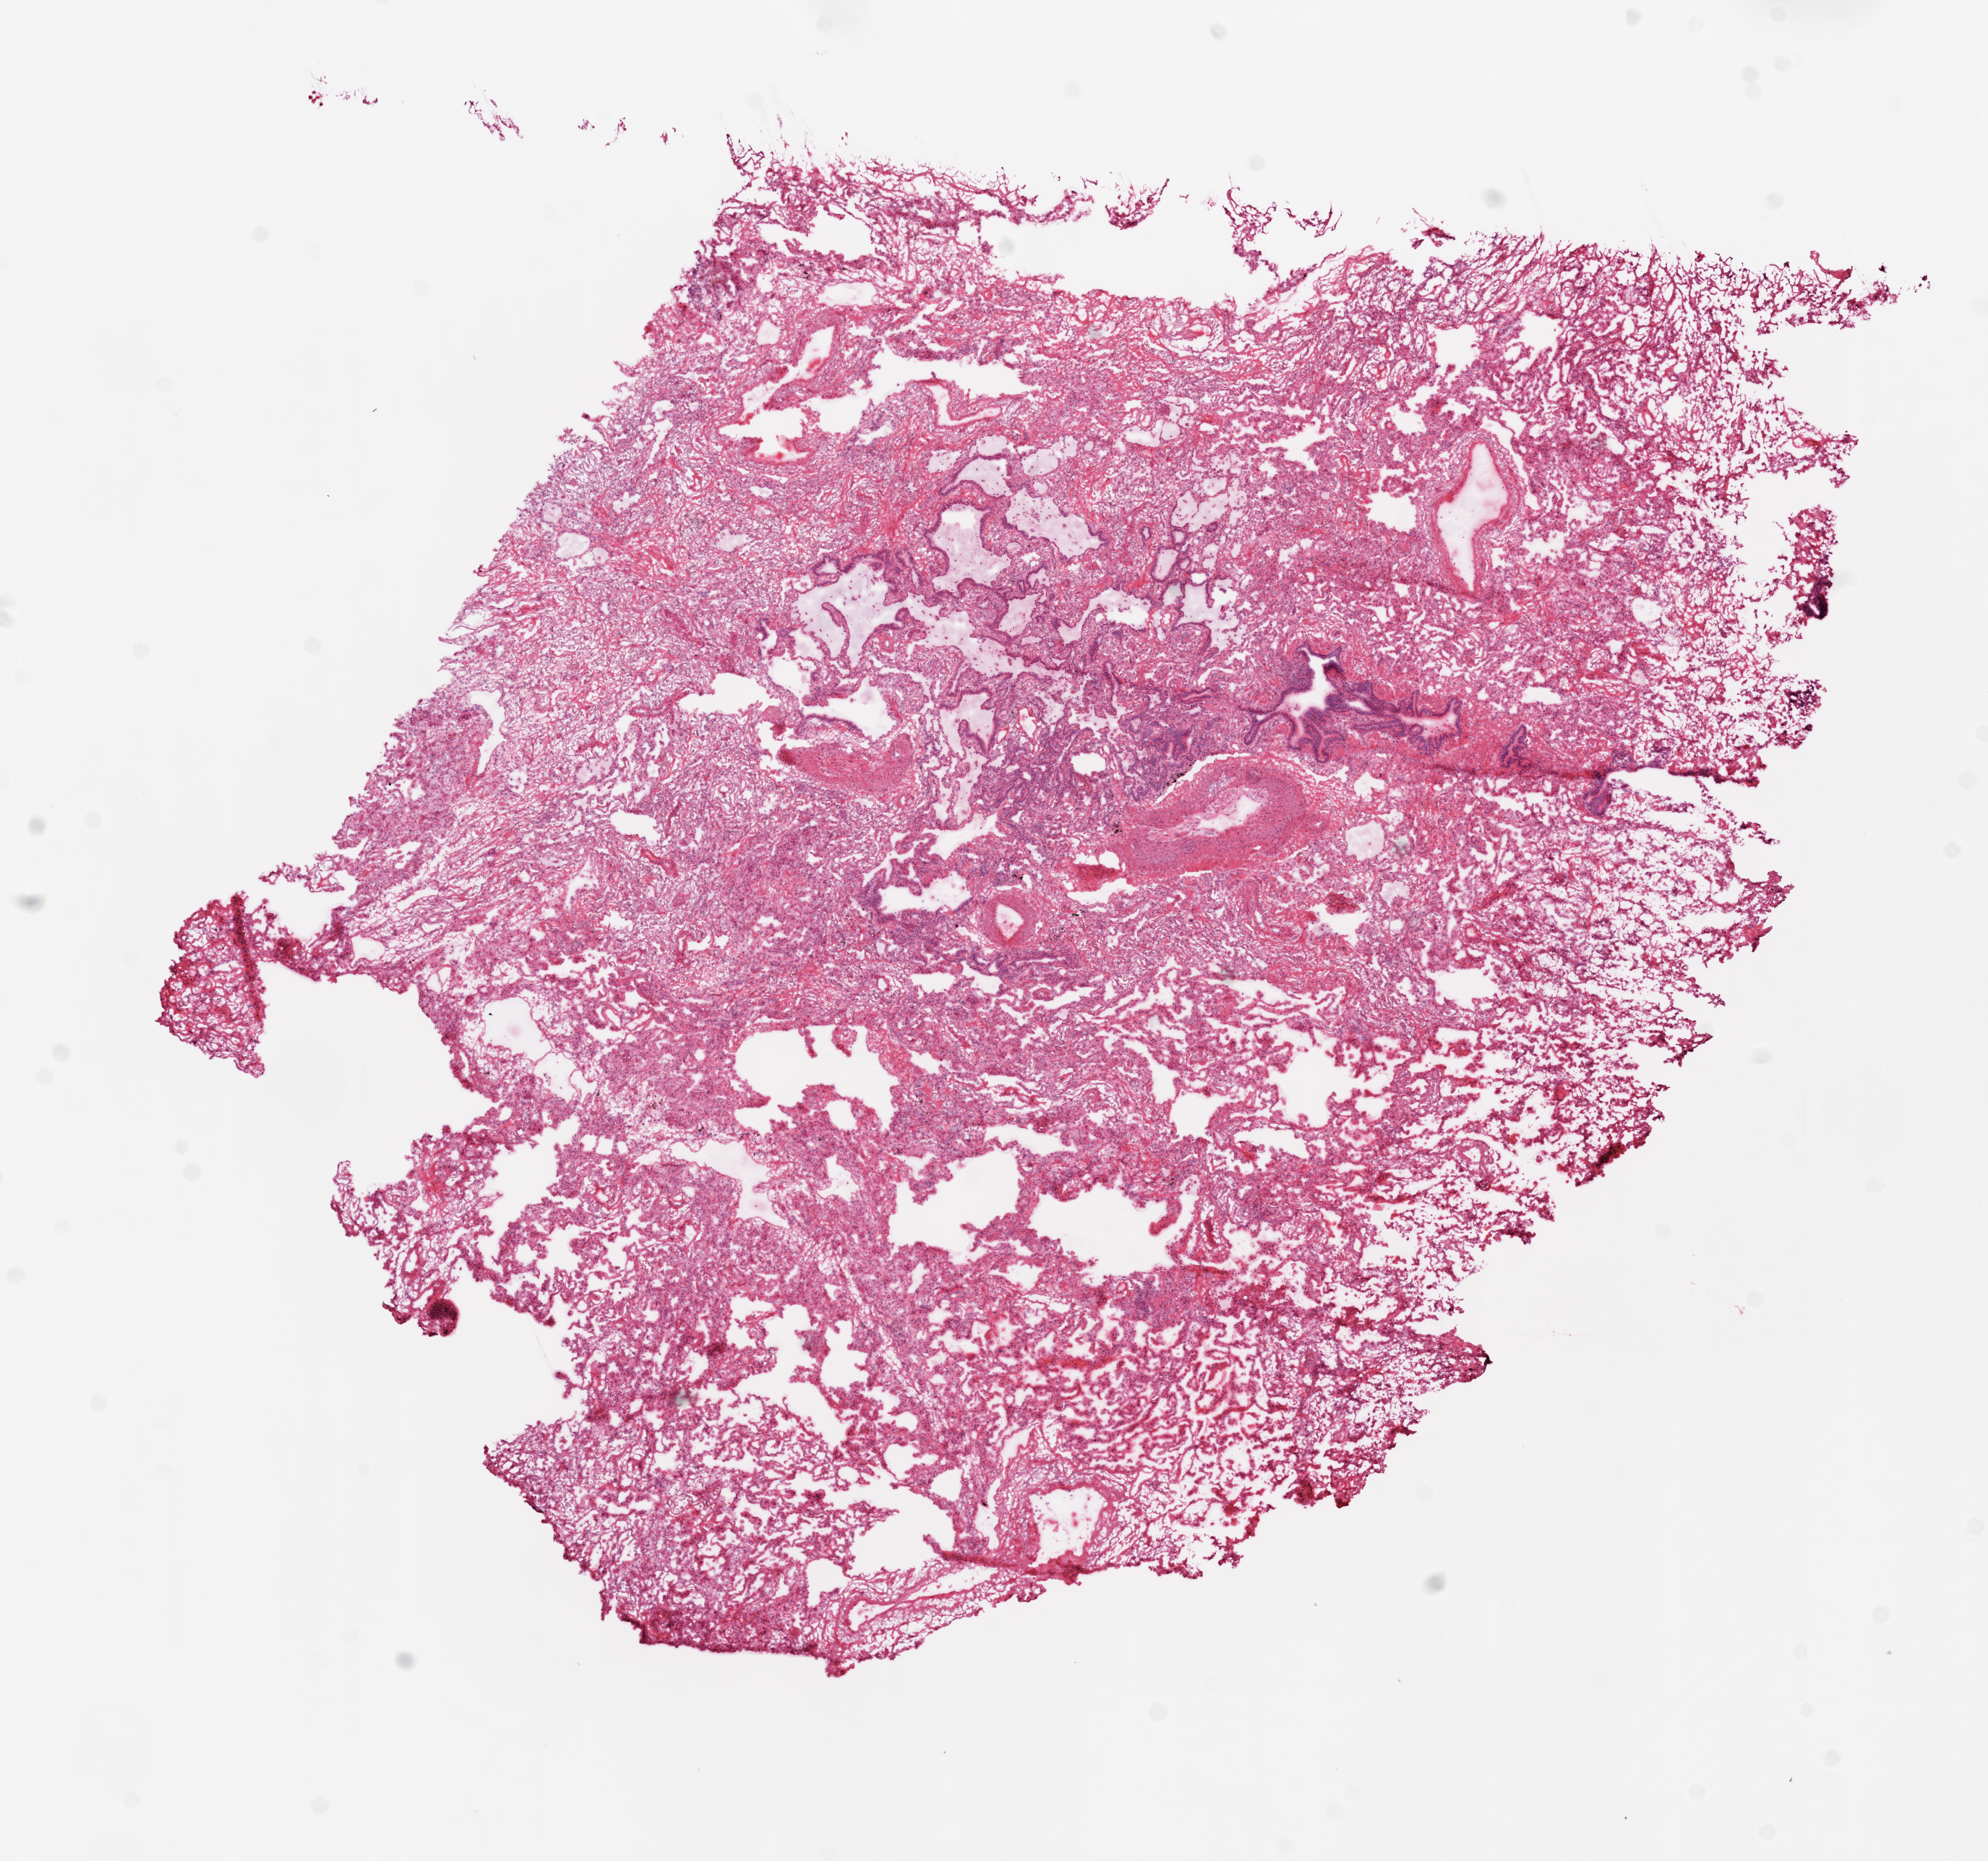
Whole-slide histology image, H&E — whole scanned area (about 11.0 x 10.3 mm, acquisition: 20x scan) shown as a low-resolution overview, frozen section from the top of the tissue portion, sample: solid tissue normal (non-tumour tissue), lung. Patient: male, age at initial diagnosis 67 years.
This section: solid tissue normal (non-tumour) sample from the same patient. Patient diagnosis: Squamous cell carcinoma, NOS.